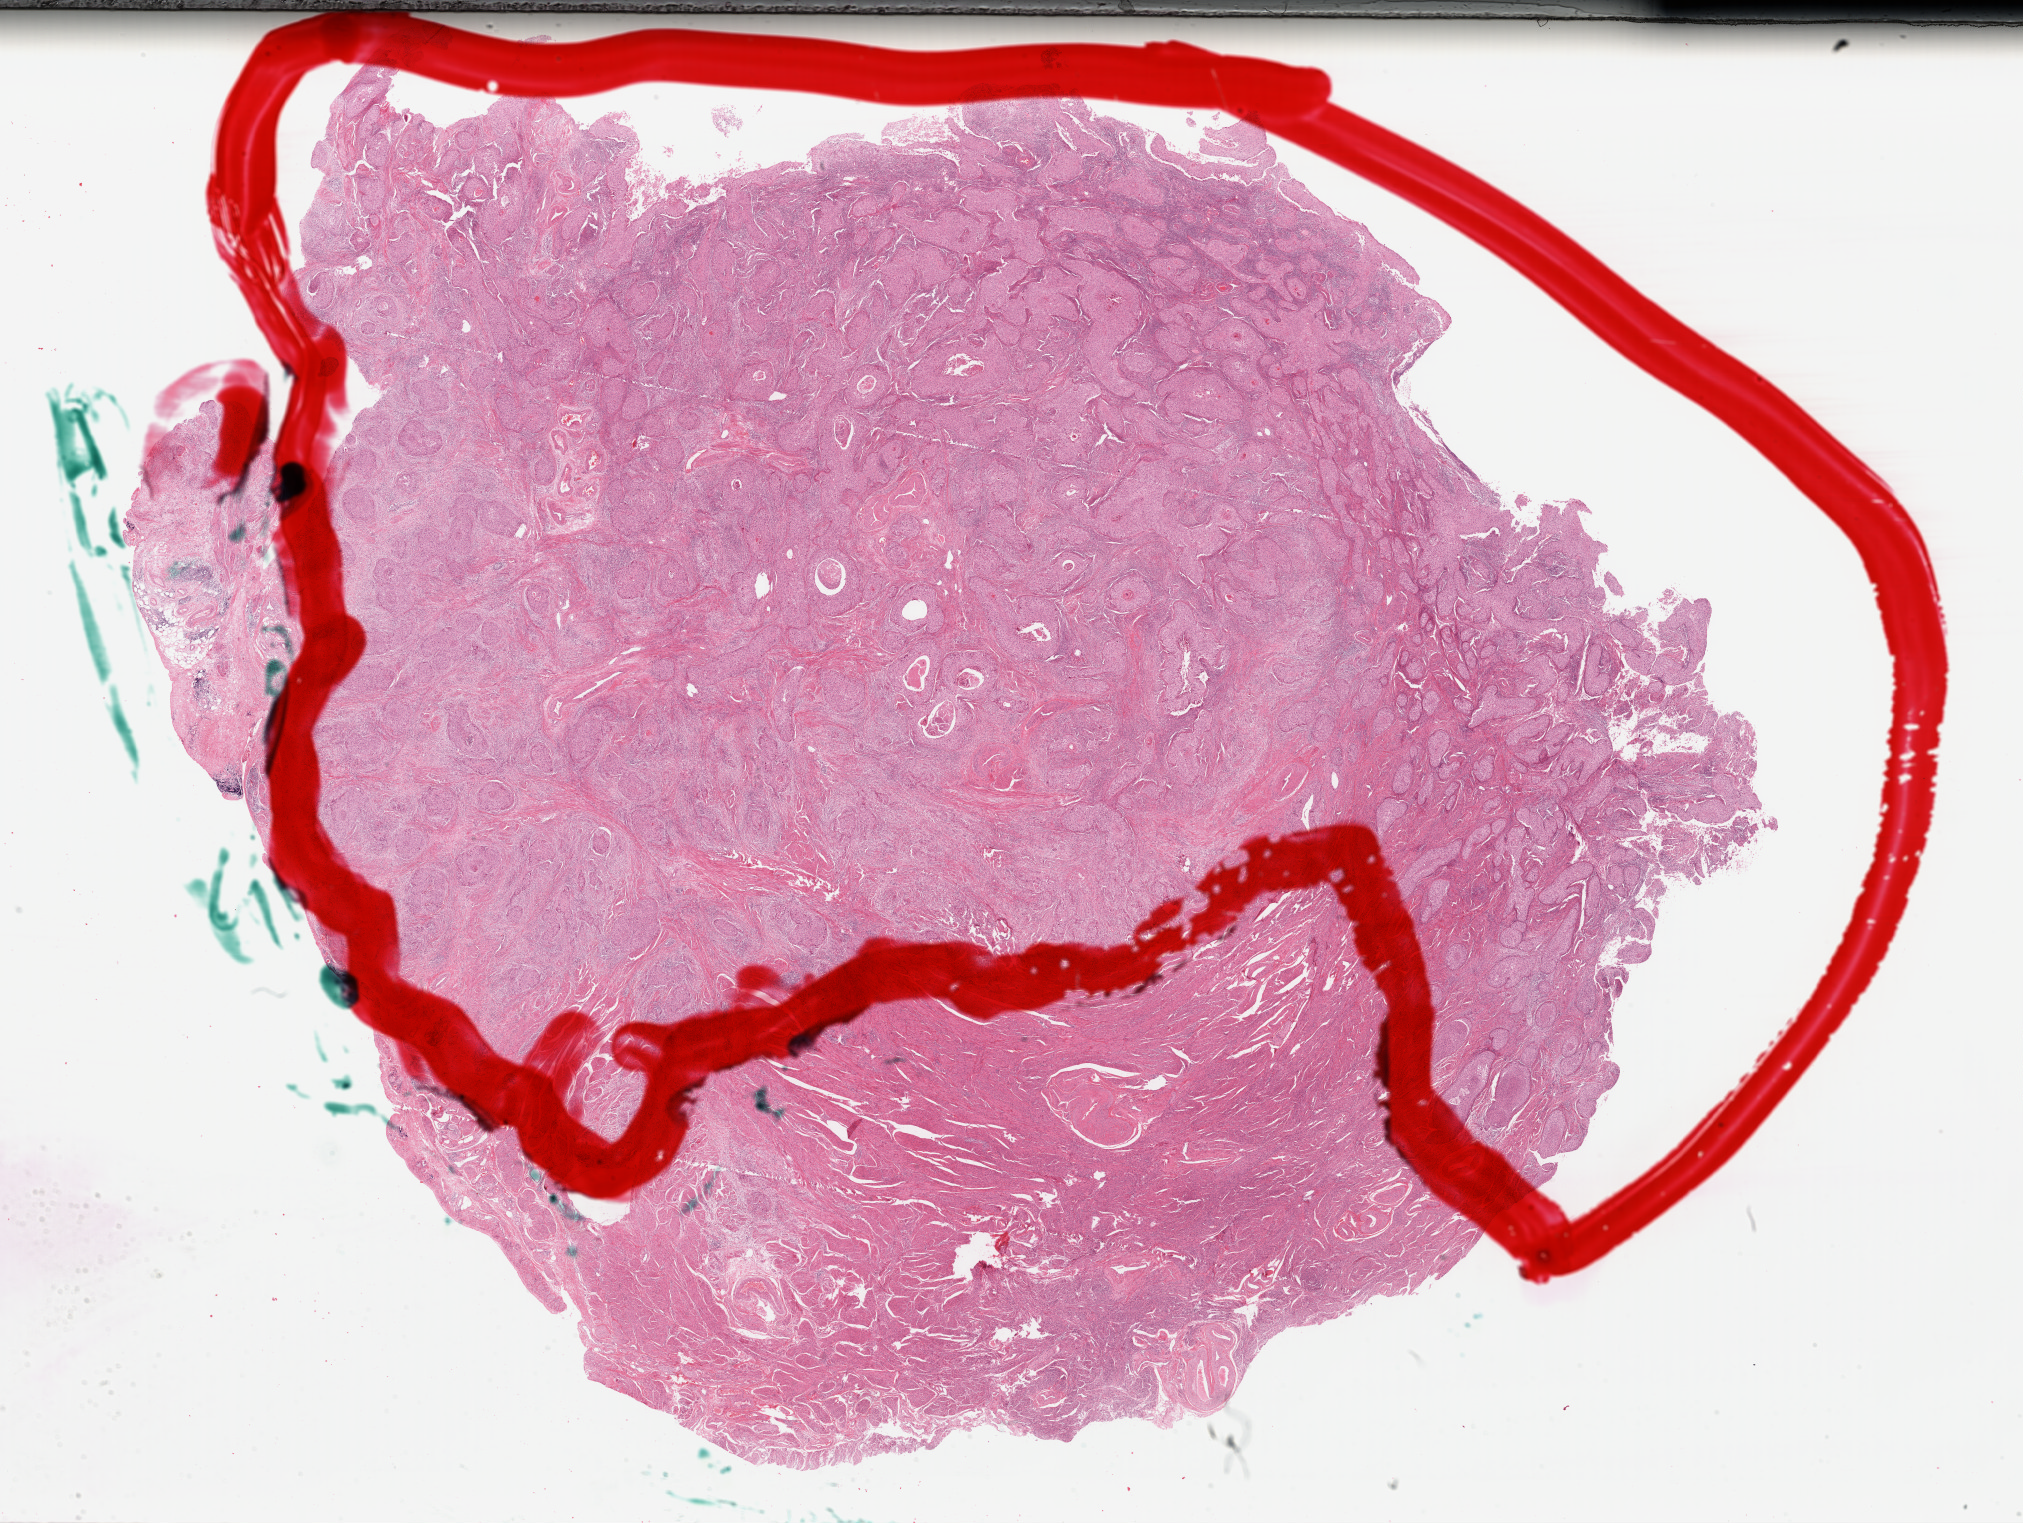
Digitized H&E-stained tissue section (whole slide), a low-resolution overview of the entire scanned area, about 31.8 x 23.9 mm (slide scanned at 40x). FFPE section. Sample: primary tumour, cervix. Patient: female, age at initial diagnosis 46 years. Histologic grade: G2 (moderately differentiated).
- lymph nodes positive (case pathology): 0 of 18 examined
- FIGO stage: IB1
- diagnosis: Squamous cell carcinoma, large cell, nonkeratinizing, NOS (cervix uteri)